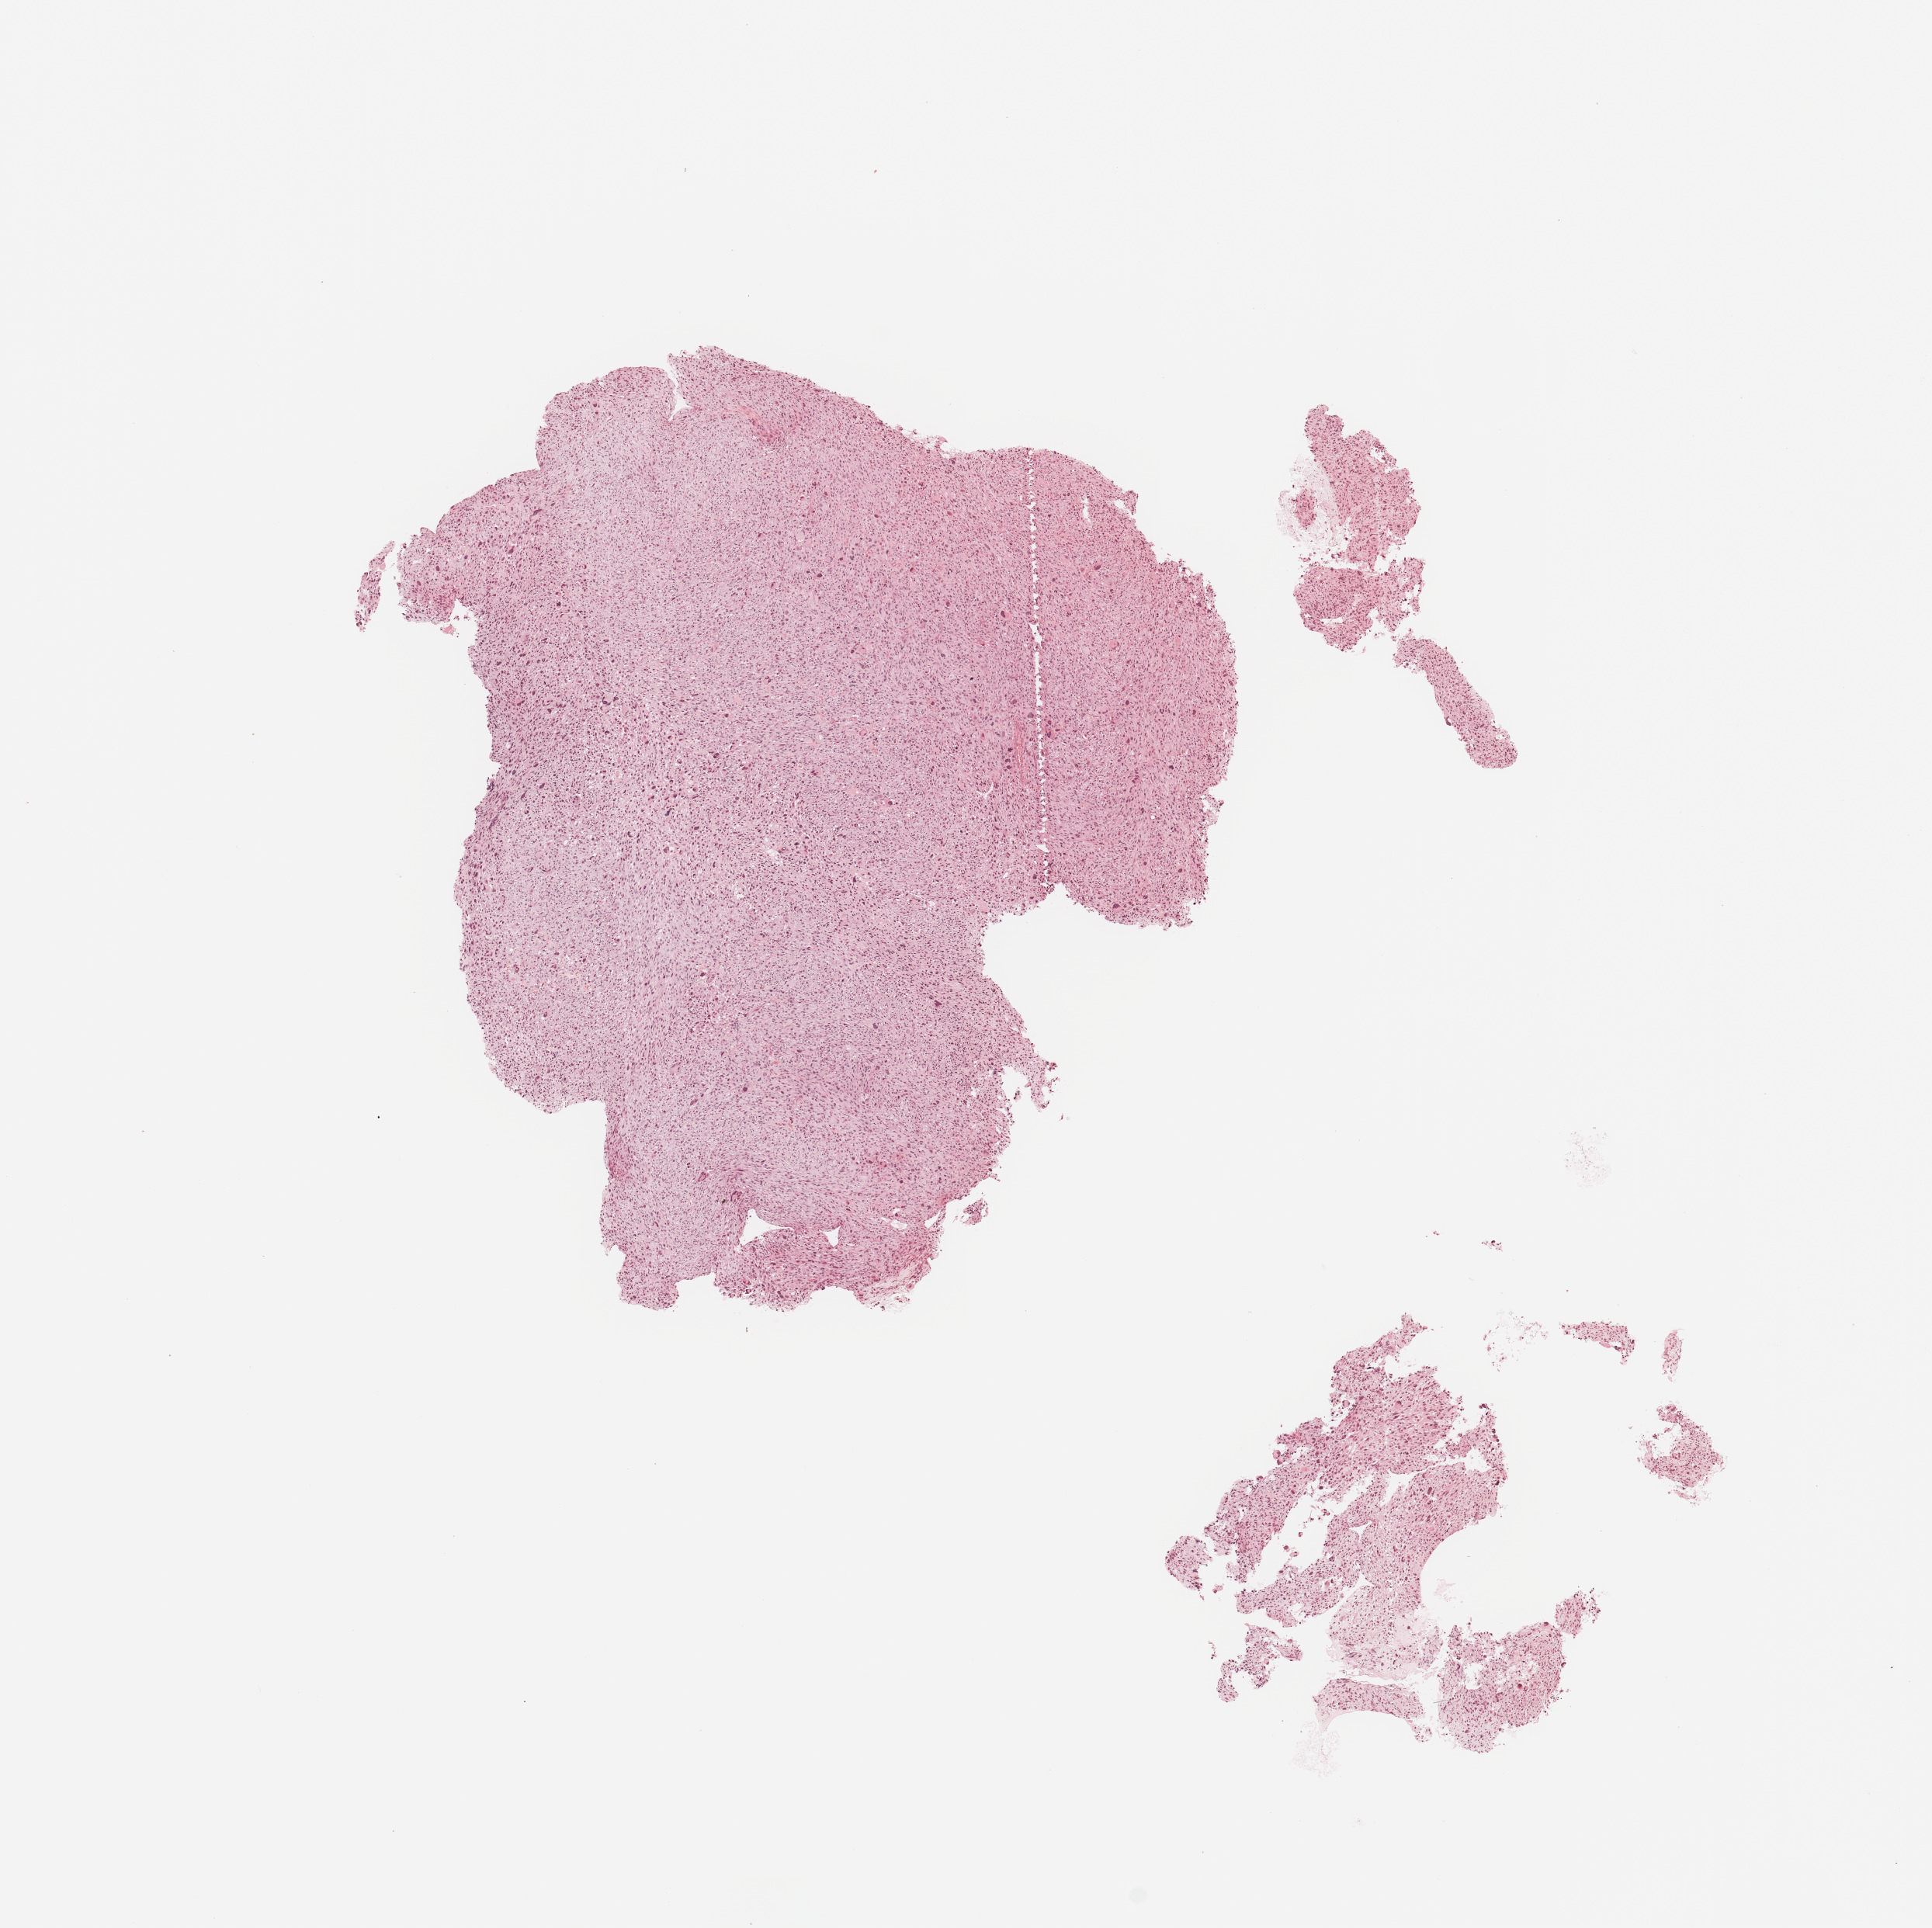
Hematoxylin and eosin (H&E) stained whole-slide image, shown as a low-resolution overview of the whole scanned area (about 9.8 x 9.8 mm, slide scanned at 20x), tumour tissue sample. Patient: female, age 48 years.
Primary tumour site (as recorded): lower extremity. Patient diagnosis (cohort enrolment): sarcoma (site not recorded at cohort level).